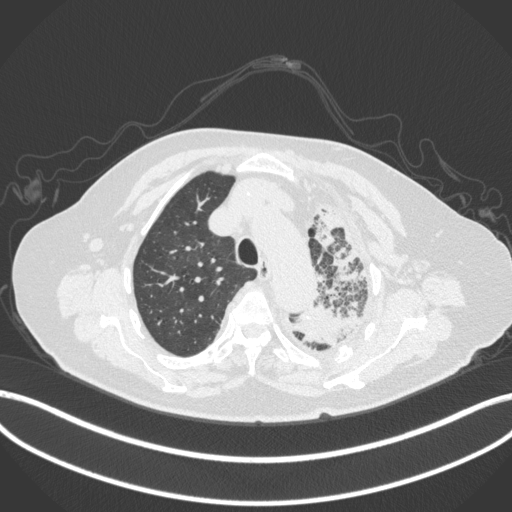
Chest CT, one axial slice. Slice 304 of 399 in the series (ordered by position). Reconstruction kernel B31f. Lung window (W 1500 / L -600 HU). 1 mm slice thickness. 512 × 512 image matrix. Patient: female, 75 years. Case-level facts recorded for this patient, not image findings: clinical TNM (as recorded): T3 N3 M1.
Structures marked on this image (rectangle marked by the reading radiologist):
- lung tumour (recorded histology: adenocarcinoma): bounding box (x1, y1, x2, y2) in pixels: (283, 297, 357, 350)